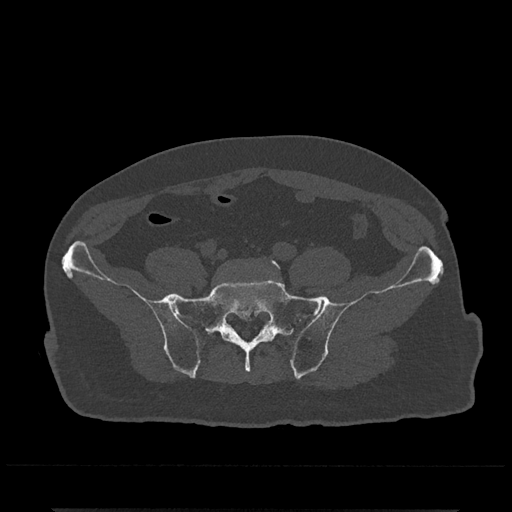
CT including the spine, one axial slice. Reconstruction kernel Br40s/3. 120 kVp. Bone window (W 1800 / L 400 HU). 512 × 512 image matrix, field of view 393 × 393 mm. Patient: male, 67 years. From the clinical record (not read from this slice): primary cancer: prostate.
Annotated regions visible in this slice (semi-automatic segmentation, software-assisted and operator-edited):
- L5 vertebra: bounding box (x1, y1, x2, y2) in pixels: (269, 259, 280, 269)